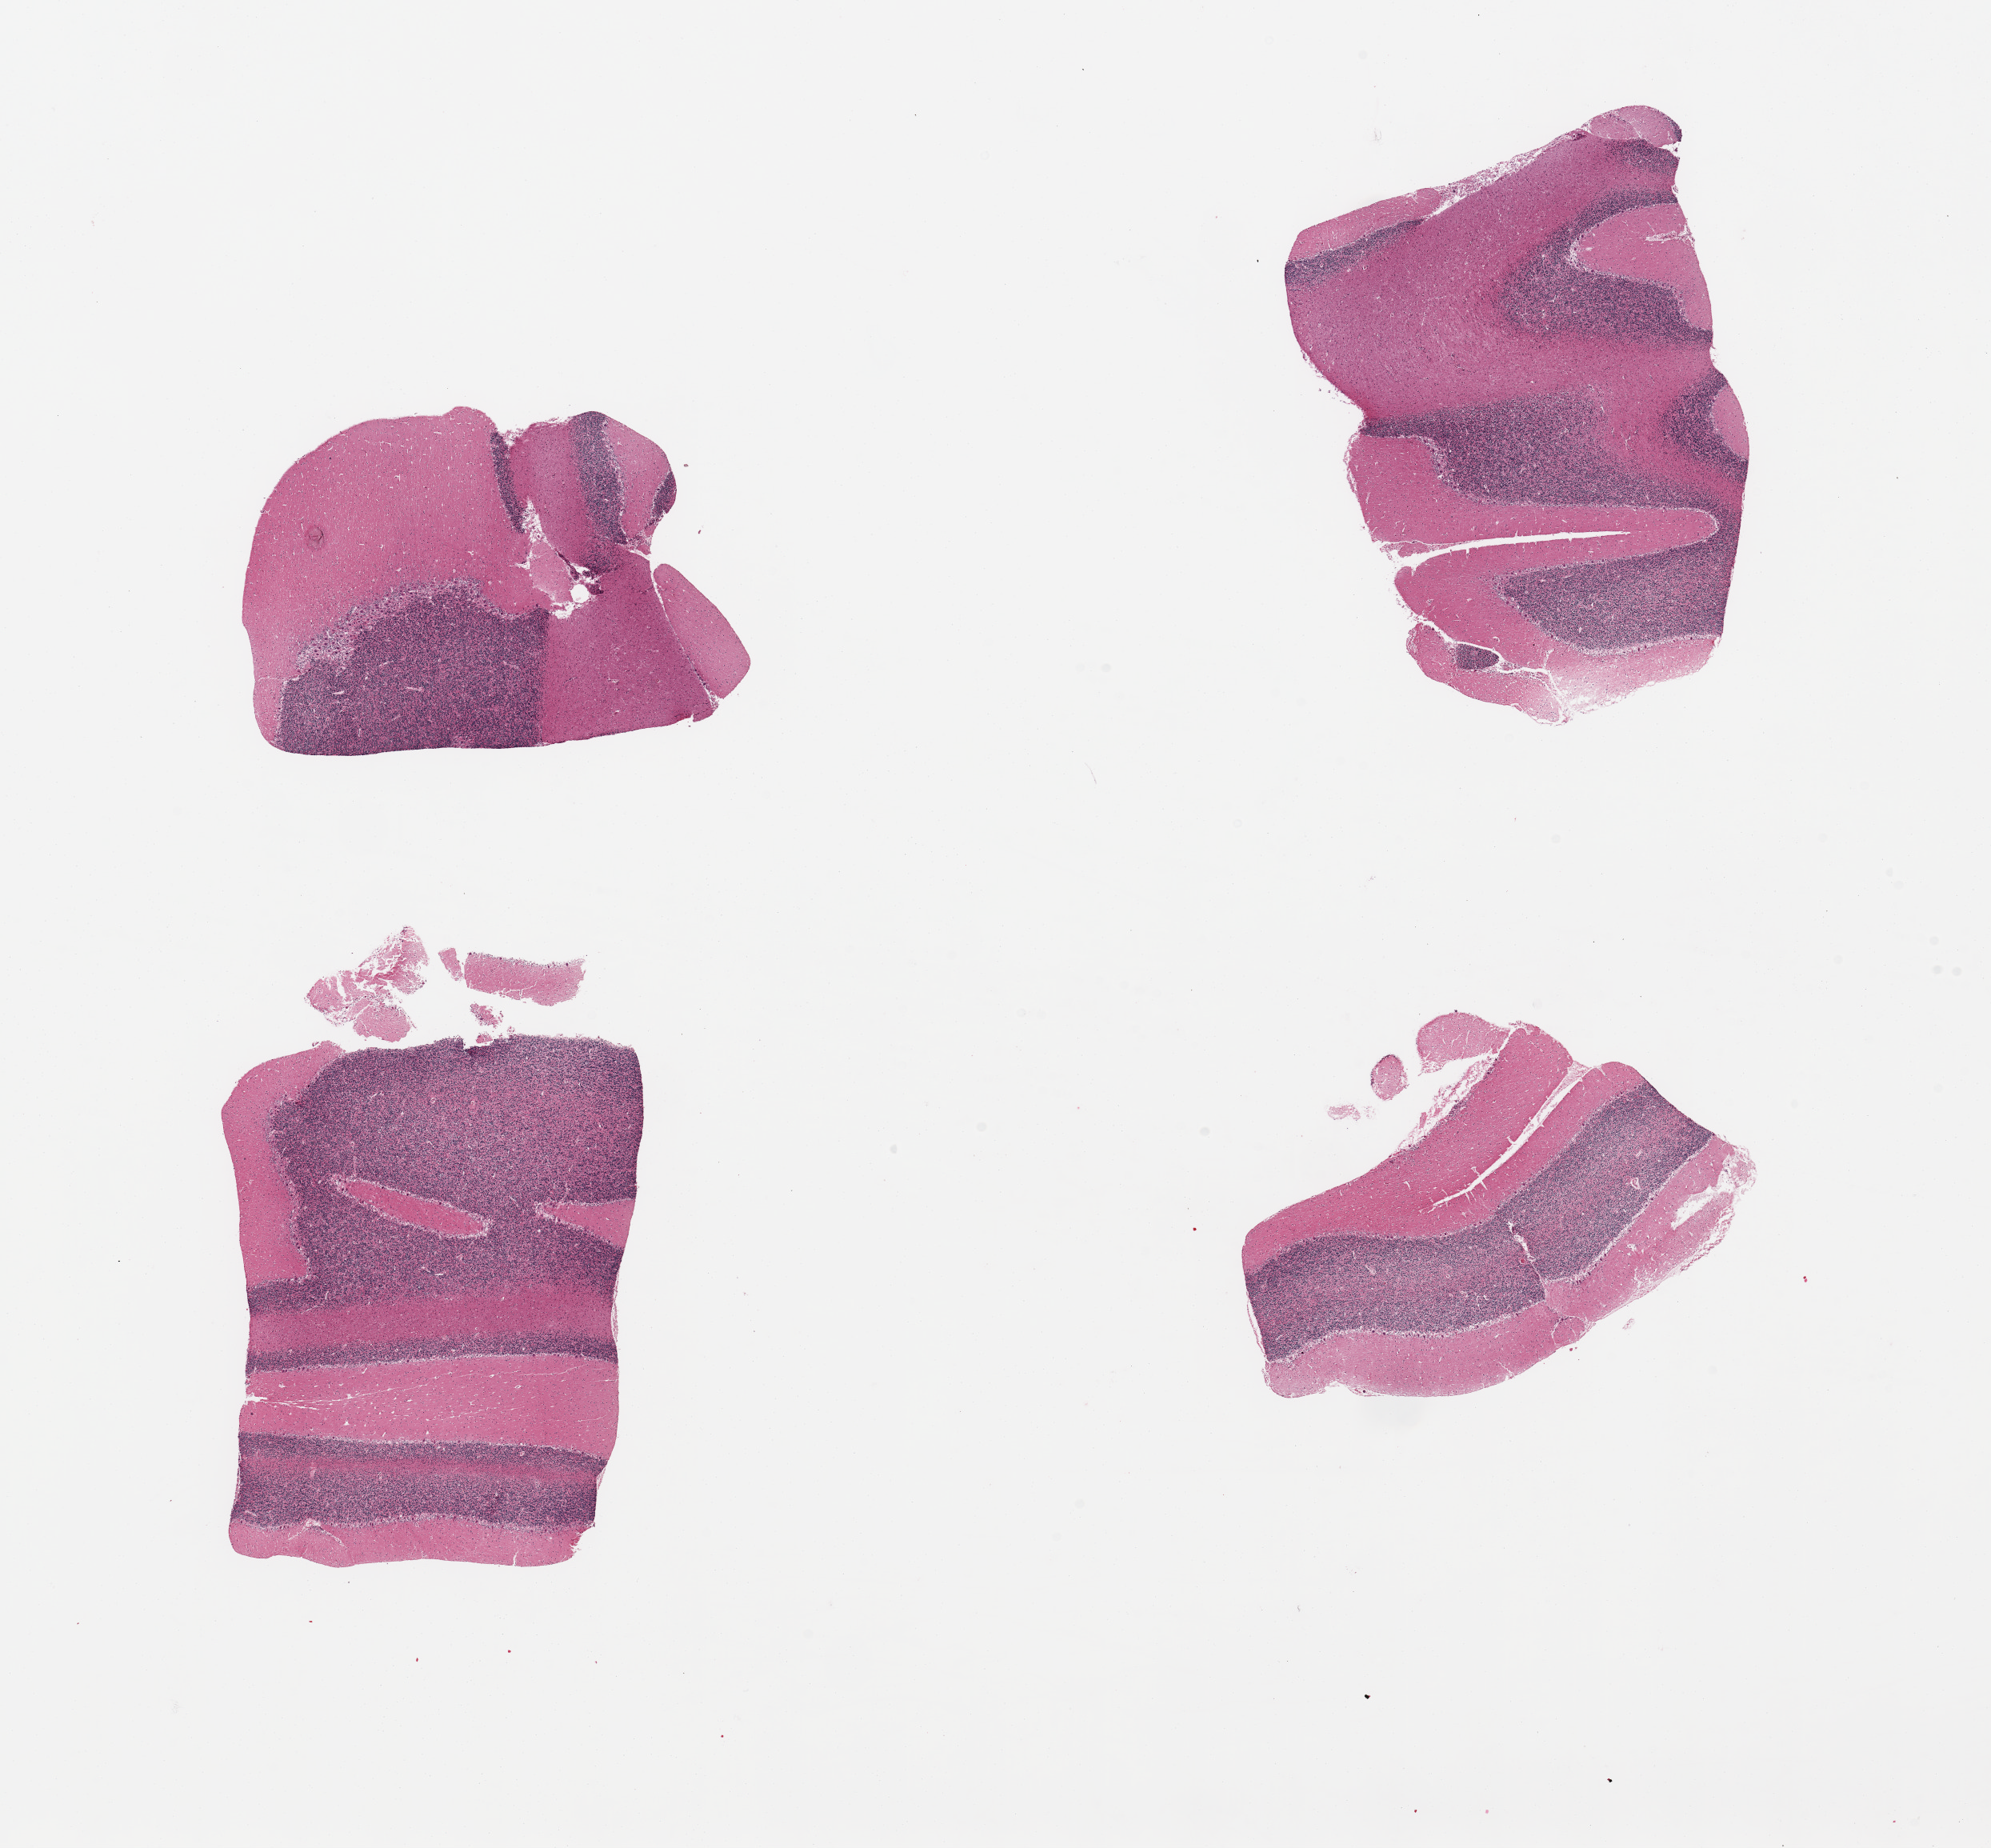
Digitized hematoxylin and eosin (H&E)-stained section, brightfield, low-resolution overview of the scanned area, about 19.7 x 18.3 mm, PAXgene-fixed paraffin-embedded (PFPE) section, target tissue: cerebellum, donor tissue sample. Donor sex: male.
• pathologist's review note for this sample: 4 pieces; mild to moderate autolysis